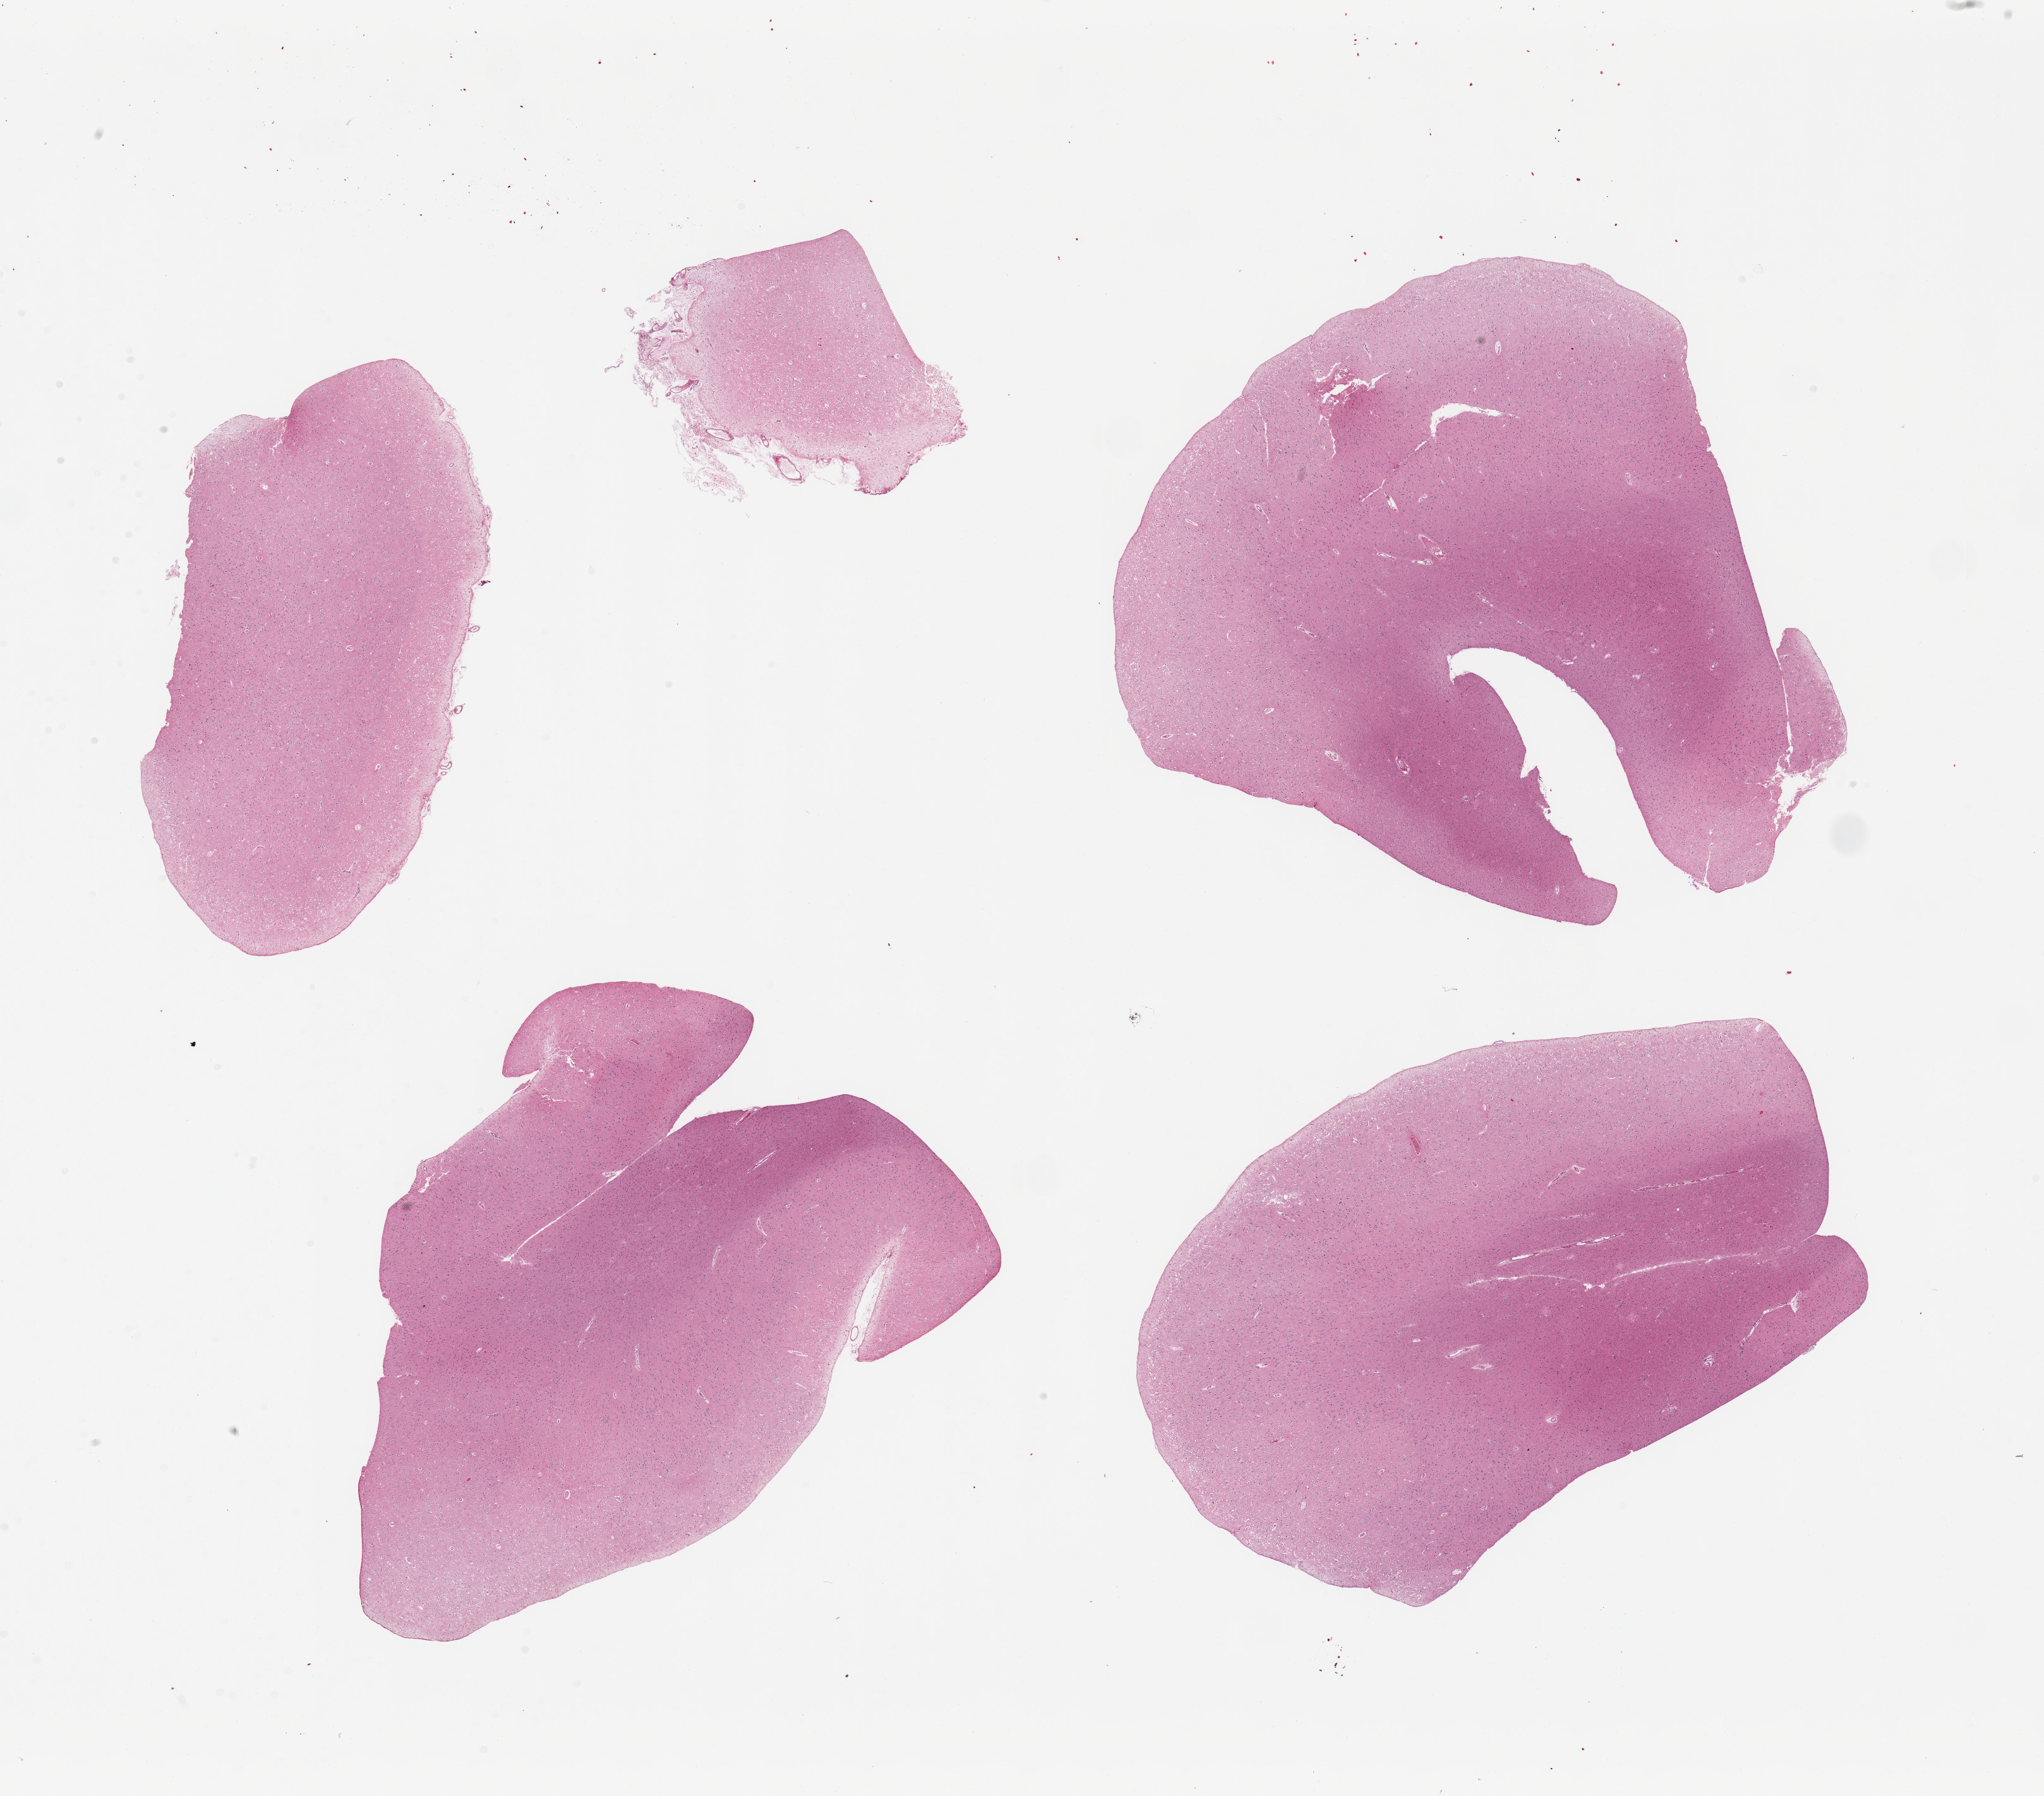
Whole-slide image, hematoxylin and eosin (H&E) stain, brightfield, low-resolution overview of the scanned area, about 25.6 x 22.5 mm (acquisition: 20x scan); PAXgene-fixed paraffin-embedded (PFPE) section; section of cerebral cortex (target tissue); donor tissue sample. Donor: male.
Review note (as recorded): 4 pieces.